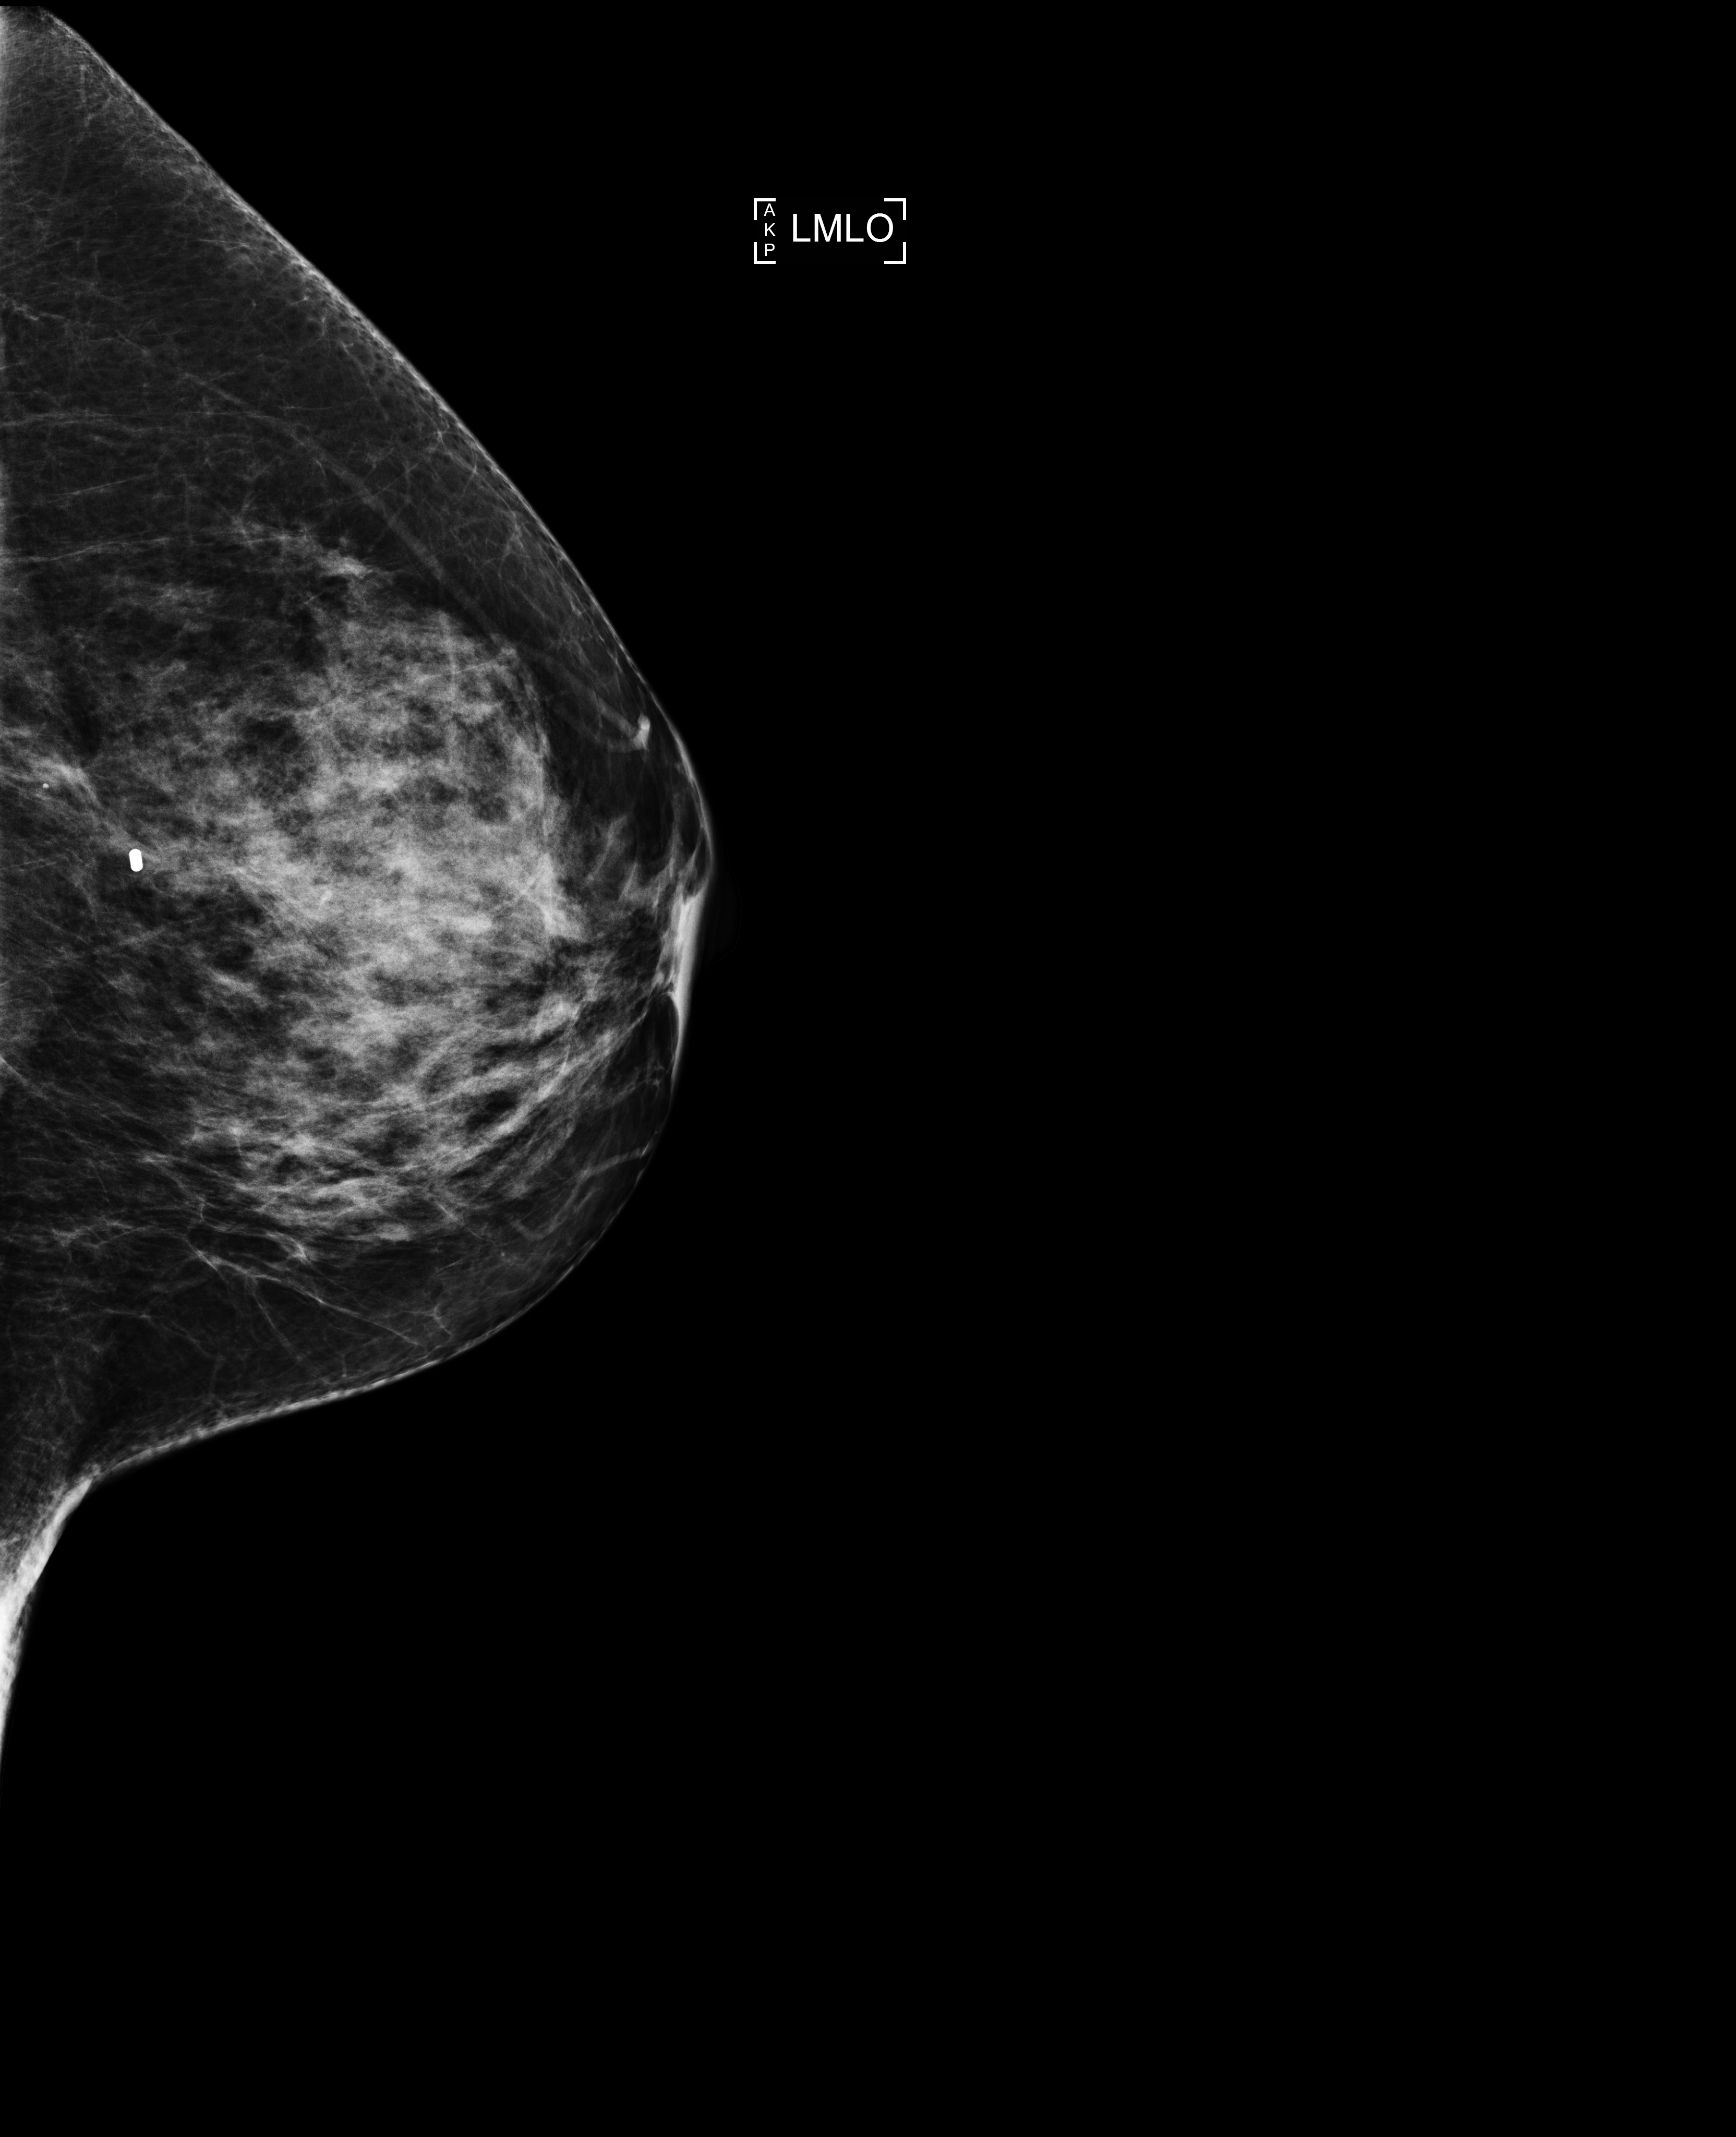
Annual screening mammography examination. Patient: female, 52 years.
Image type: full-field digital mammogram. Breast: left. Projection: MLO view.